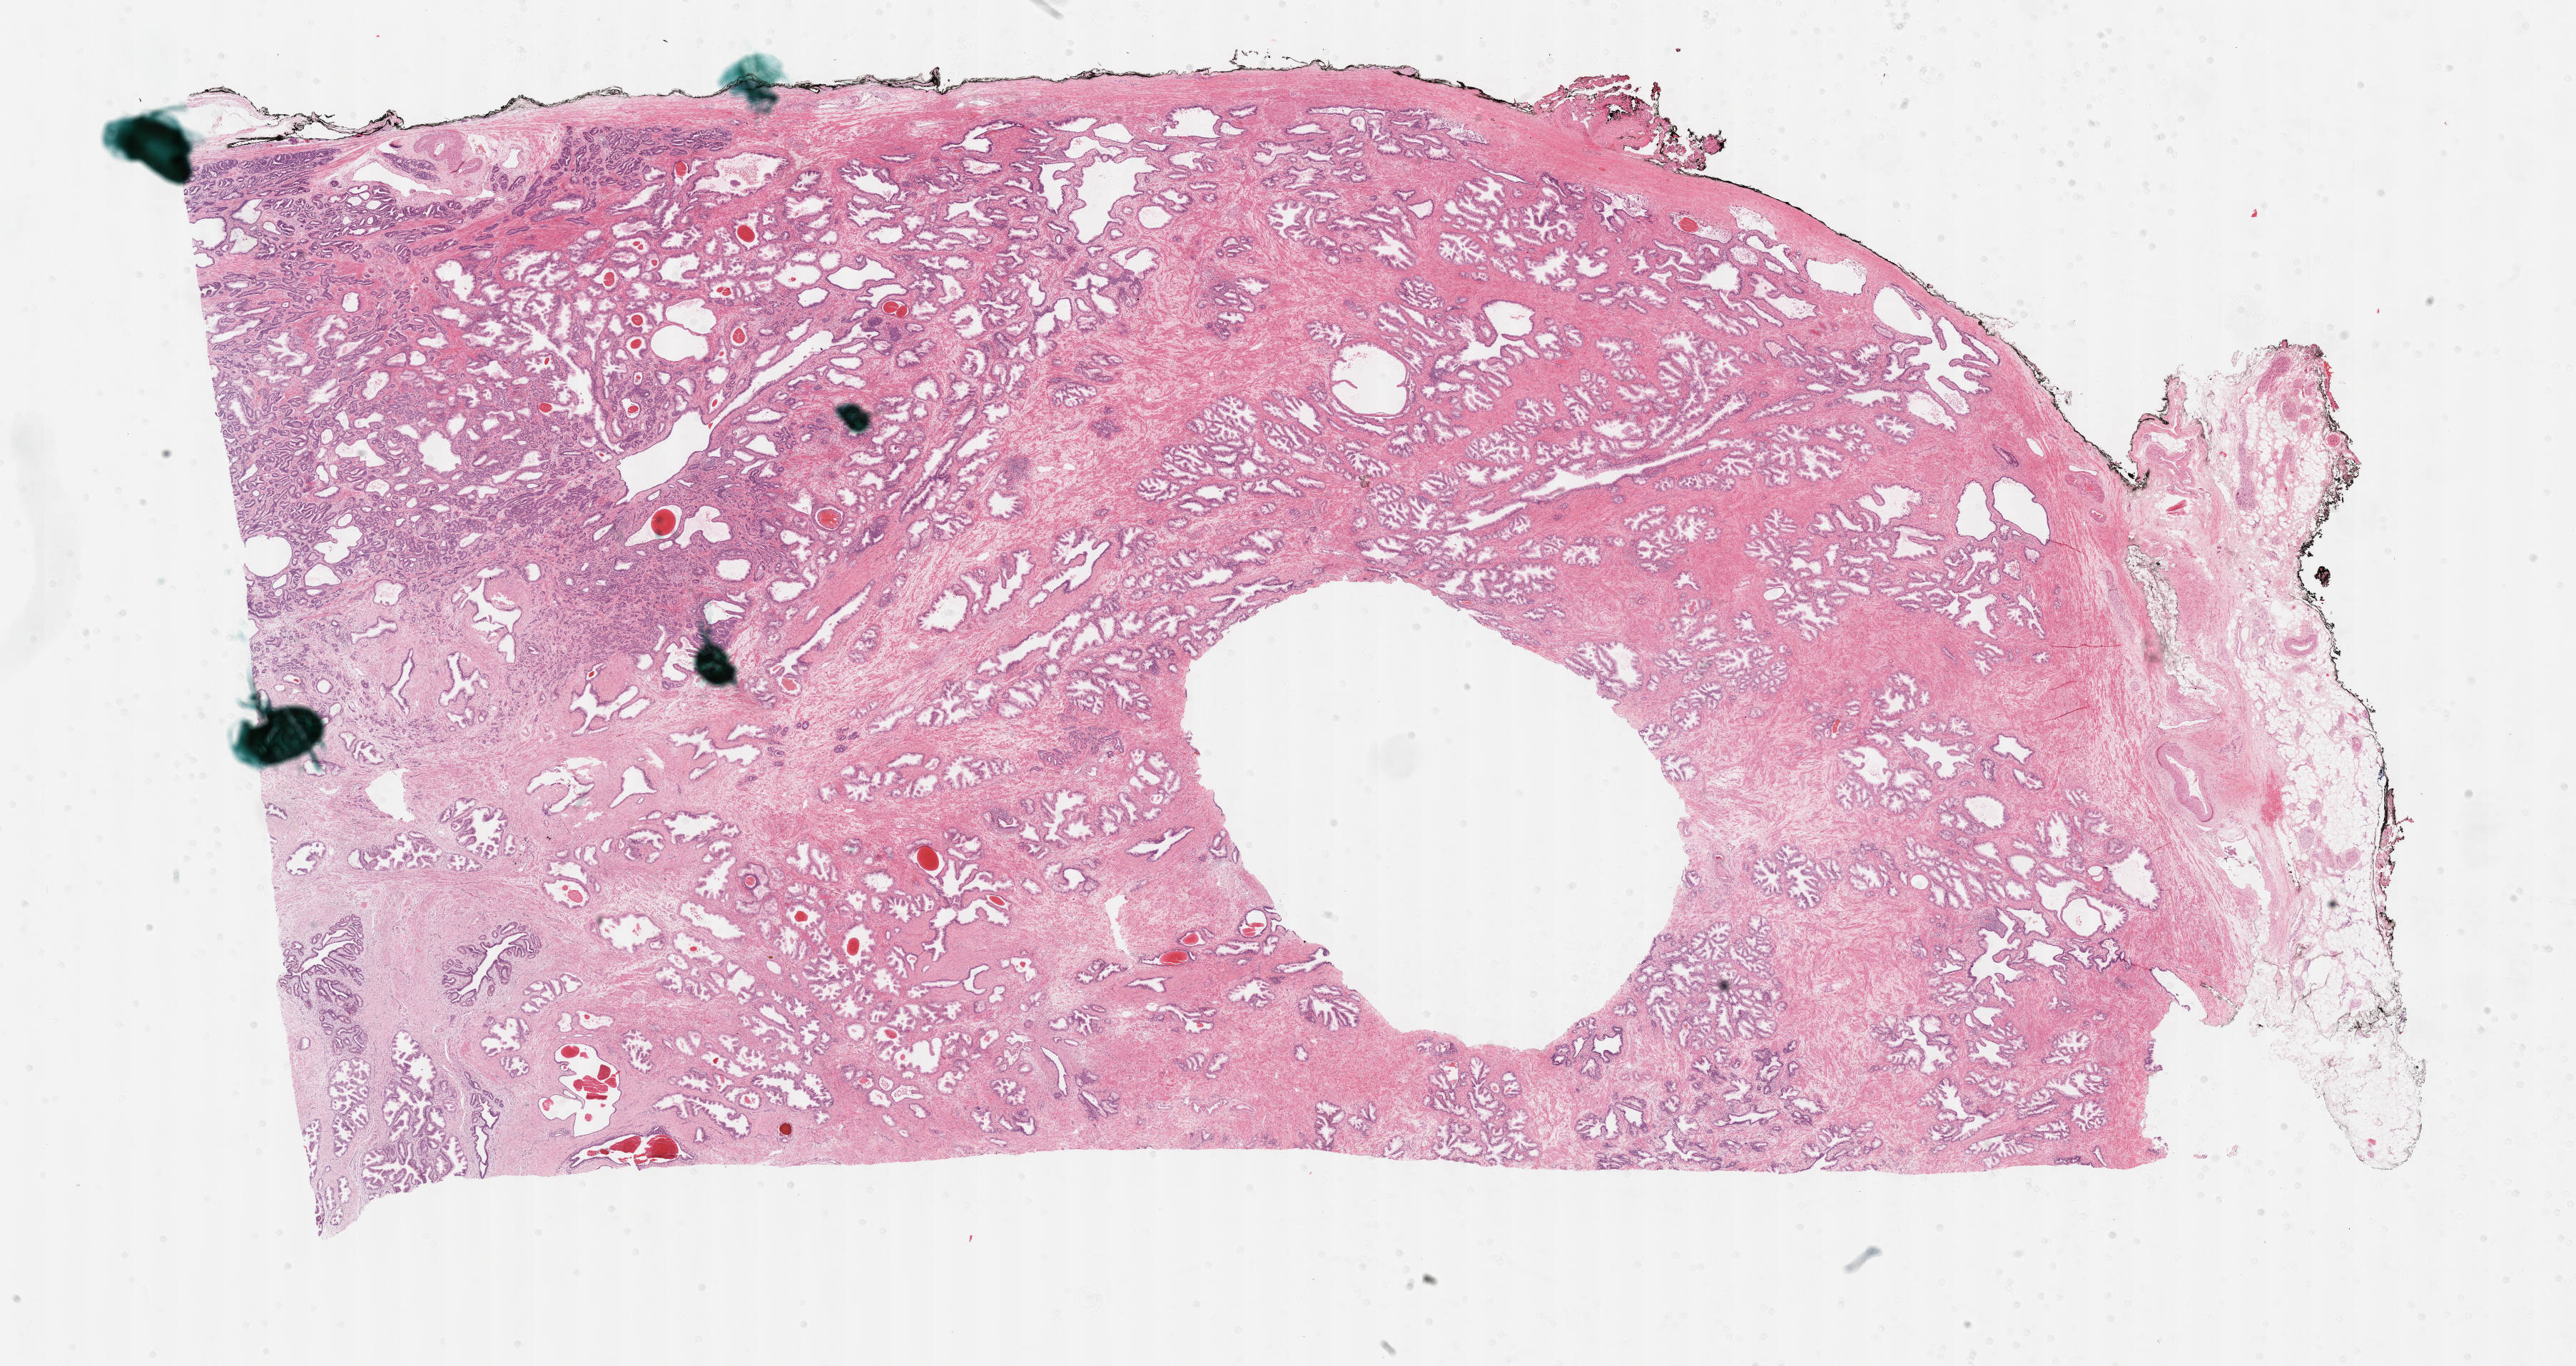
Whole-slide histology image, H&E-stained, shown as a low-resolution overview of the whole scanned area (about 29.2 x 15.5 mm, from a 40x scan), formalin-fixed paraffin-embedded (FFPE) diagnostic section, prostate, primary tumour sample. Patient: male, age at initial diagnosis 56 years. Gleason score: 6 (3+3).
Laterality: bilateral. Pathologic diagnosis: Adenocarcinoma, NOS.